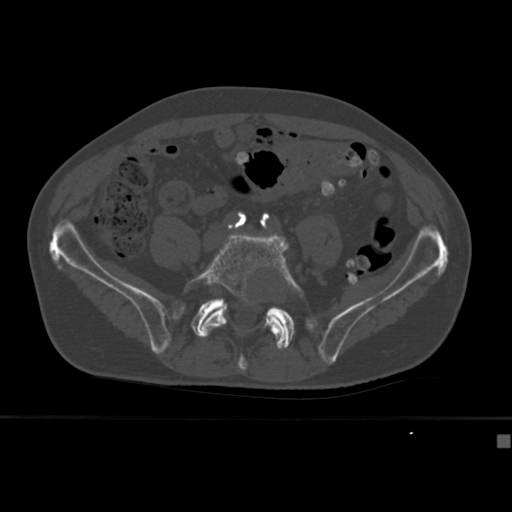
CT including the spine, one axial slice; position 83 of 430 along the scan axis; bone window (W 1800 / L 400 HU); 1.5 mm slice thickness; 512 × 512 image matrix, field of view 337 × 337 mm. Male patient, age 64 years. From the clinical record (not read from this slice): primary cancer: uterus; vertebrae with lytic lesions (as recorded): T1, T4, T5, T7, L5.
Outlined on this slice (semi-automatically segmented with operator editing):
- L5 vertebra: box from (x=184, y=233) to (x=304, y=350) px